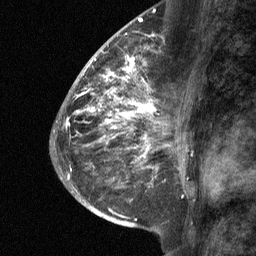
Breast MRI (dynamic contrast-enhanced), one sagittal slice; slice 36 of 64 in the series (ordered by position); dynamic contrast-enhanced study with each time point stored as its own series, time point 2 of 3 at this slice position (early post-contrast, ordered by acquisition time); 1.5 T; TE 4.8 ms, TR 27 ms; 2 mm slice thickness; 256 × 256 image matrix, field of view 180 × 180 mm. Female patient, age 59 years. From the clinical record (not read from this slice): setting: breast cancer imaged before/during neoadjuvant chemotherapy; receptor status: triple-negative.
Annotated regions visible in this slice (semi-automatic segmentation, software-assisted and operator-edited):
- analysis volume of interest (the breast-tissue region the enhancement analysis was run in; not a lesion): box from (x=122, y=58) to (x=176, y=109) px
- tumour enhancement mask (voxels above the 90 % enhancement threshold inside the analysis volume of interest): (x=122, y=58)–(x=157, y=109)